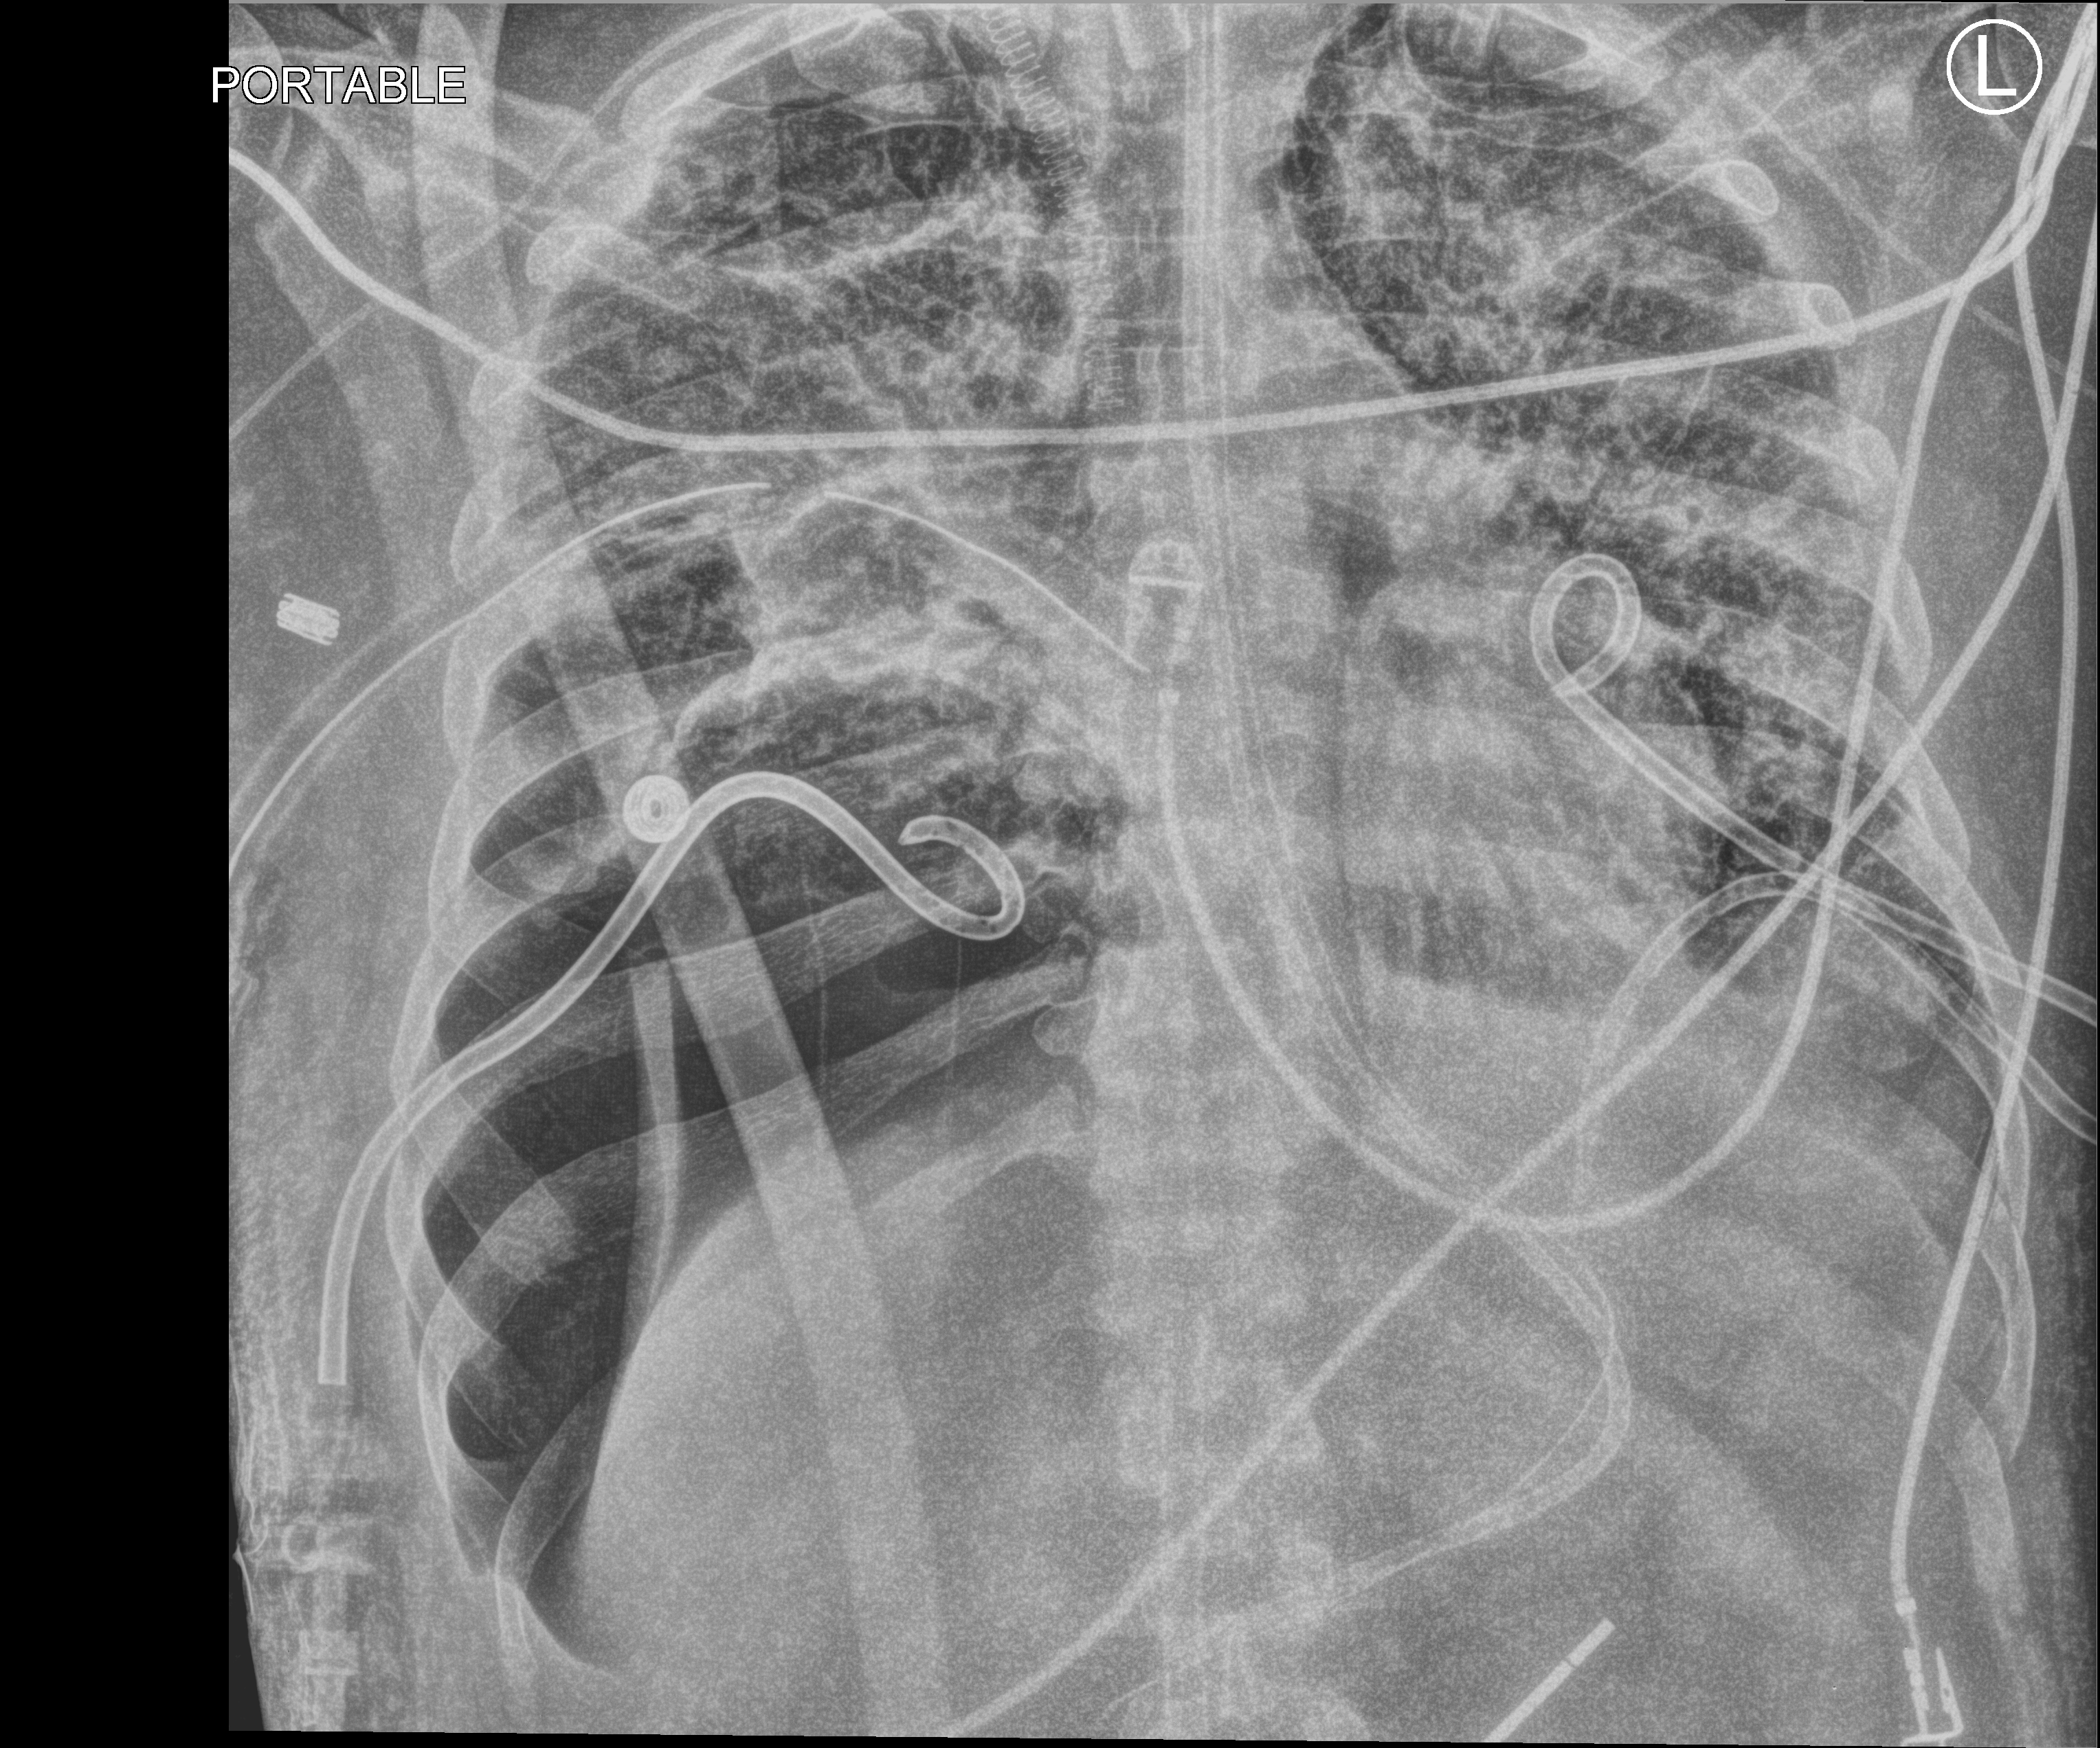
Portable chest radiograph; anteroposterior (AP) projection. Adult patient hospitalised with COVID-19, age 18–59 years.
Admission-level facts for this patient (not findings on this image; timing relative to this image not recorded):
- diabetes (admission record): no
- mechanically ventilated during this hospital stay: yes